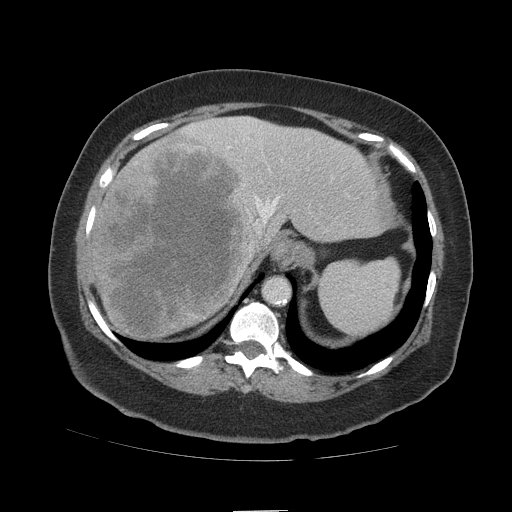
Contrast-enhanced abdominal CT (liver protocol), one axial slice. Slice 84 of 109 in the series (ordered by position). Reconstruction kernel STANDARD. Soft-tissue window (W 400 / L 40 HU). 512 × 512 image matrix. Case-level facts recorded for this patient, not image findings: diagnosis: hepatocellular carcinoma (patient treated with transarterial chemoembolisation; whether this scan precedes or follows treatment is not stated here); TNM stage (as recorded): Stage-IVB; Child-Pugh class: A; tumour differentiation: poorly differentiated.
Structures marked on this image (semi-automatically segmented with operator editing):
- liver parenchyma outside the tumour (the mass and vessels are separate outlines, so this box may not span the whole liver): bounding box (x1, y1, x2, y2) in pixels: (89, 116, 392, 338)
- mass: (94, 135, 263, 337)
- liver vessels: (187, 120, 279, 224)